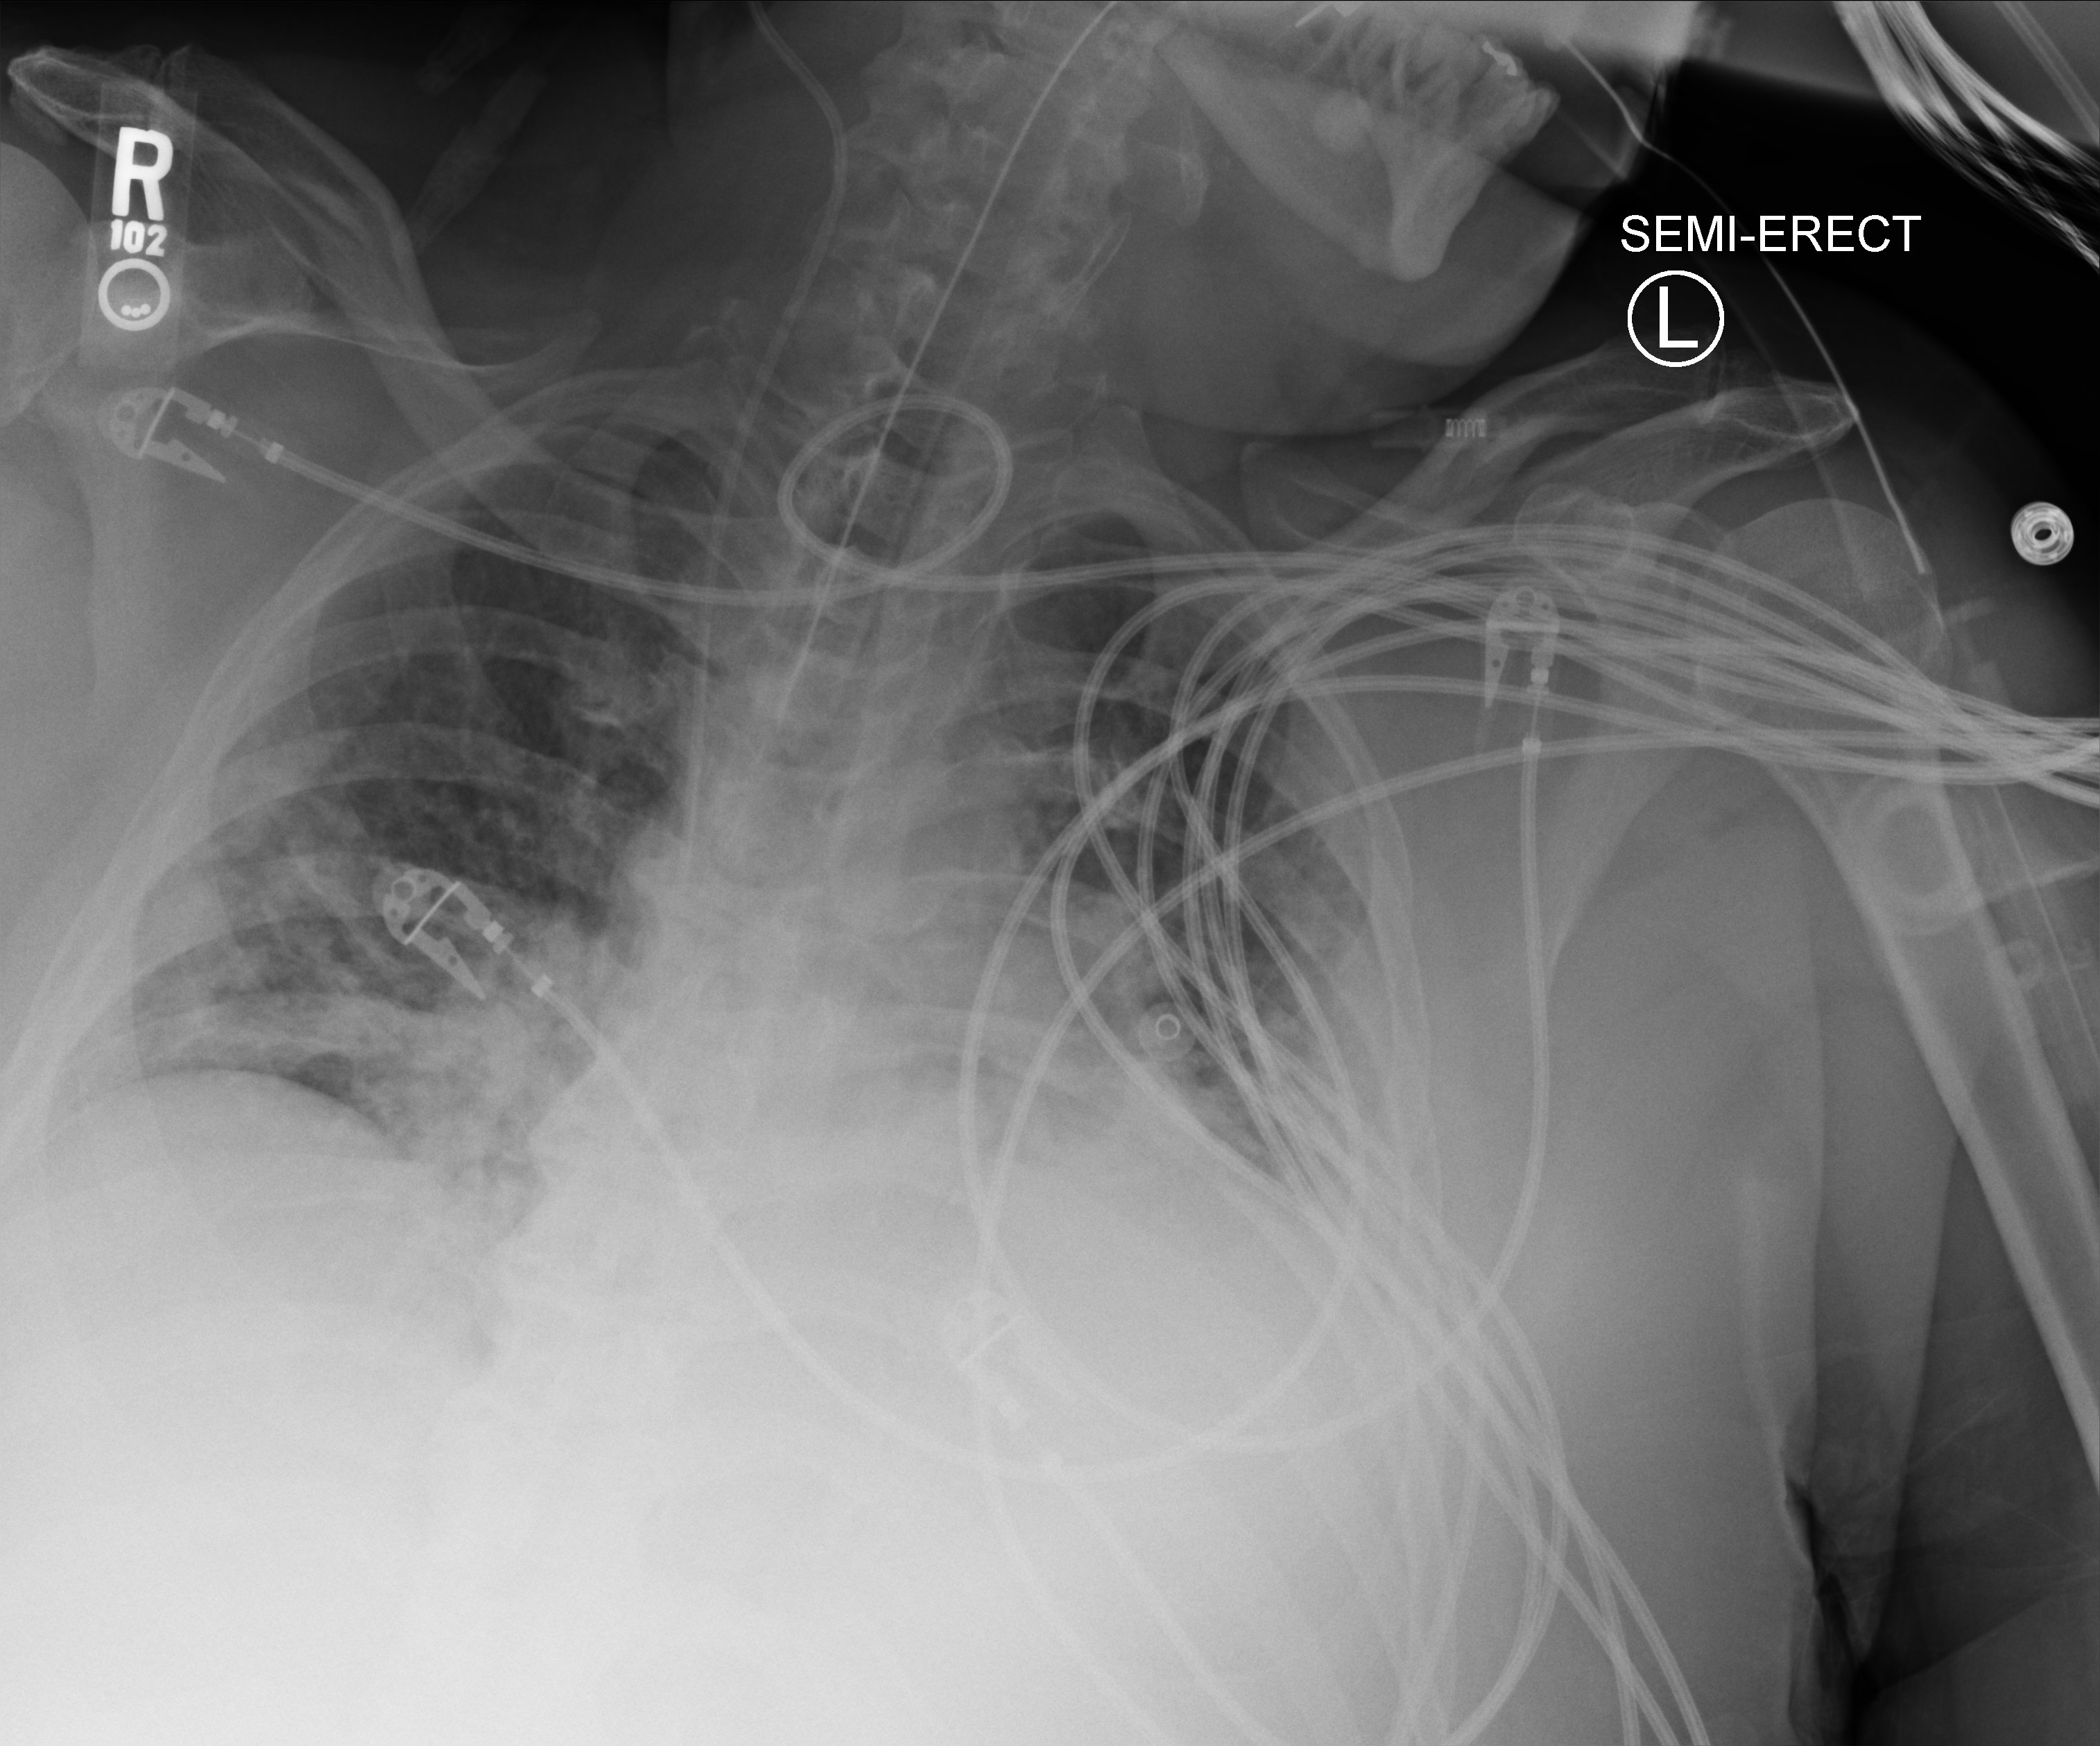
Bedside chest radiograph (computed radiography), anteroposterior (AP) projection. Patient hospitalised with COVID-19; male, aged 18–59 years.
Admission-level facts for this patient (not findings on this image; timing relative to this image not recorded): other chronic lung disease (admission record): no; mechanically ventilated during this hospital stay: yes.